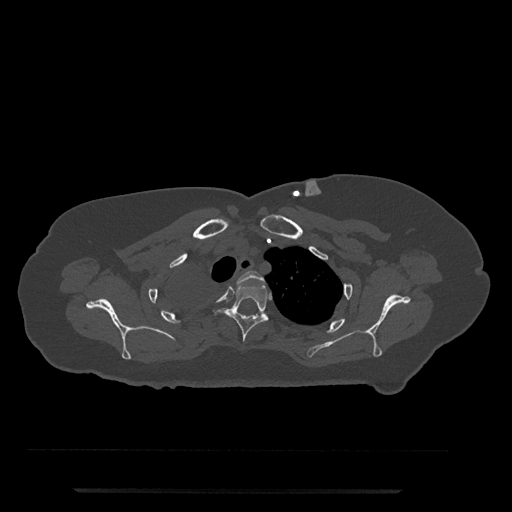
CT including the spine, one axial slice; position 634 of 797 along the scan axis; reconstruction kernel Br40s/3; 120 kVp; bone window (W 1800 / L 400 HU); 512 × 512 image matrix. Female patient, age 51 years. Case-level facts recorded for this patient, not image findings: primary cancer: neuro.
Annotated regions visible in this slice (semi-automatically segmented with operator editing):
- T2 vertebra: box from (x=237, y=271) to (x=264, y=282) px
- T3 vertebra: (x=213, y=283)–(x=269, y=342)